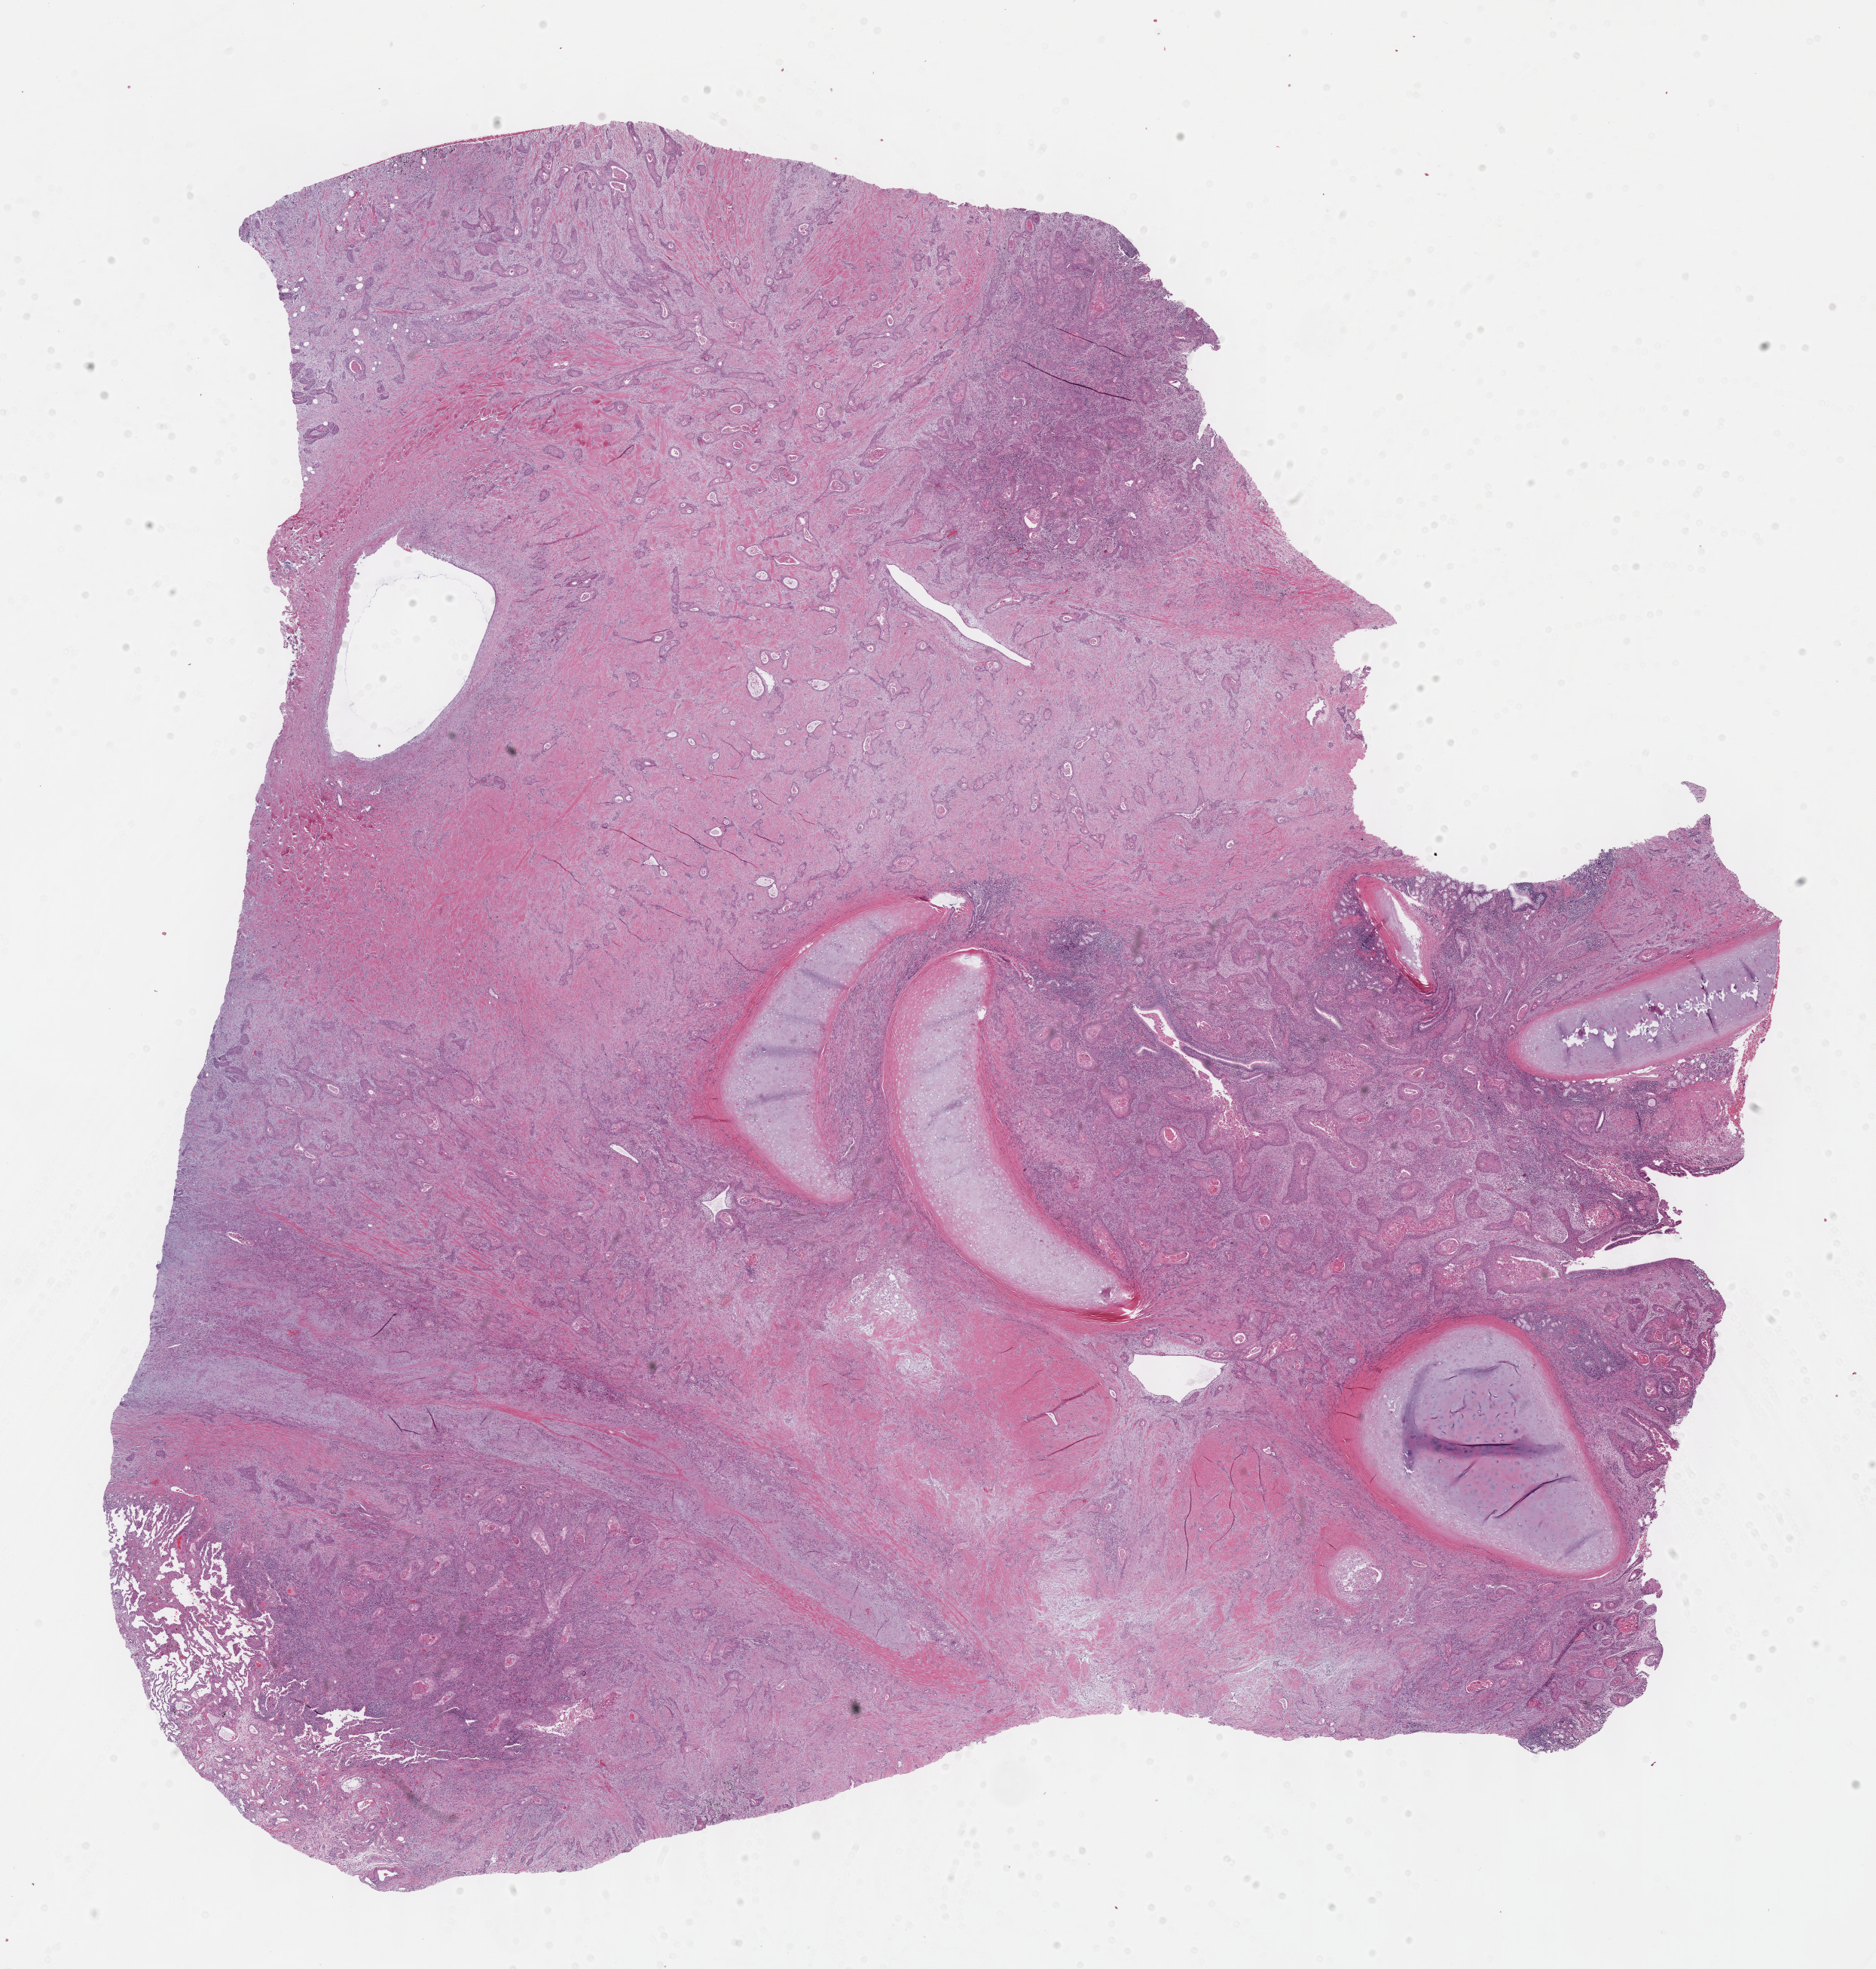
H&E whole-slide image, a low-resolution overview of the entire scanned area, about 20.1 x 21.1 mm. Formalin-fixed paraffin-embedded (FFPE) diagnostic section. Primary tumour sample from the lung. Male, age 76 years at initial diagnosis.
AJCC pathologic stage: IB (7th edition). Laterality: right. Diagnosis: Squamous cell carcinoma, NOS.